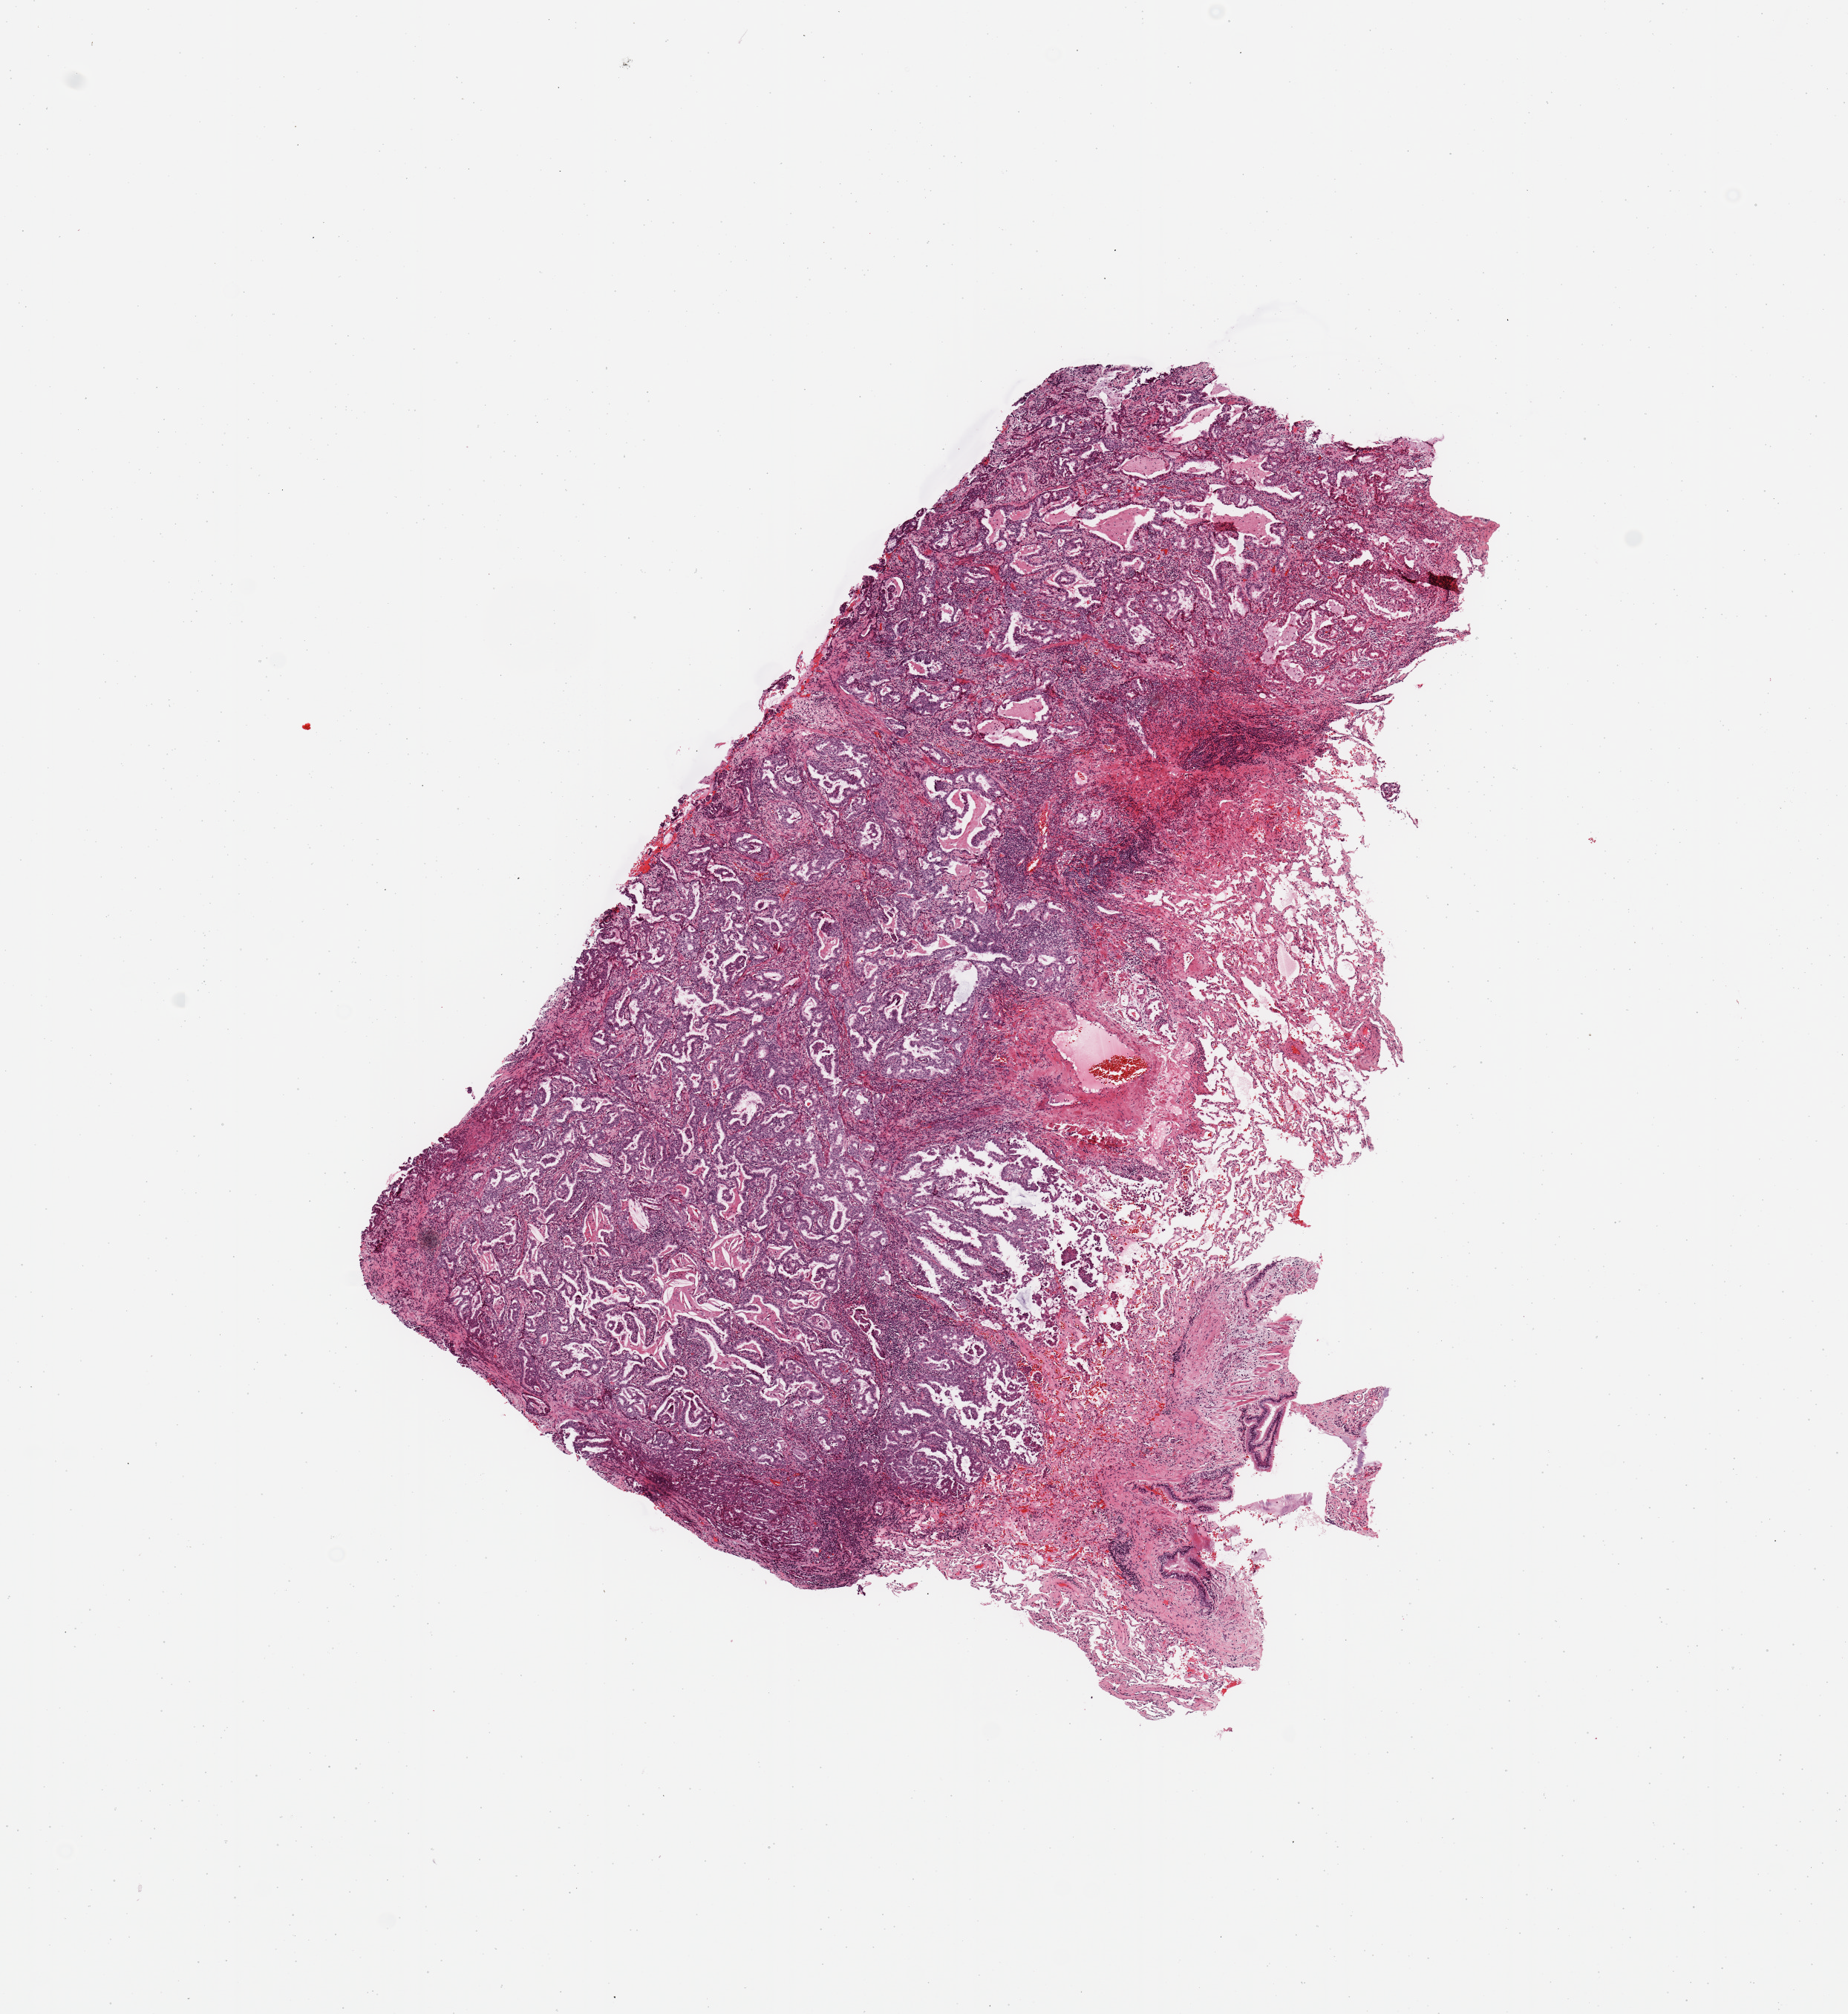
H&E whole-slide image — low-resolution overview of the scanned area, about 9.8 x 10.7 mm (acquisition: 20x scan), tumour tissue sample, sampled site: lung. Patient: female, age 61 years. Histologic grade: G2 (moderately differentiated). Slide review estimates, as recorded: tumour nuclei 65%, necrosis 5%.
Primary tumour site (as recorded): right upper lobe. Diagnosis: Adenocarcinoma, NOS. AJCC pathologic stage: IIIA.